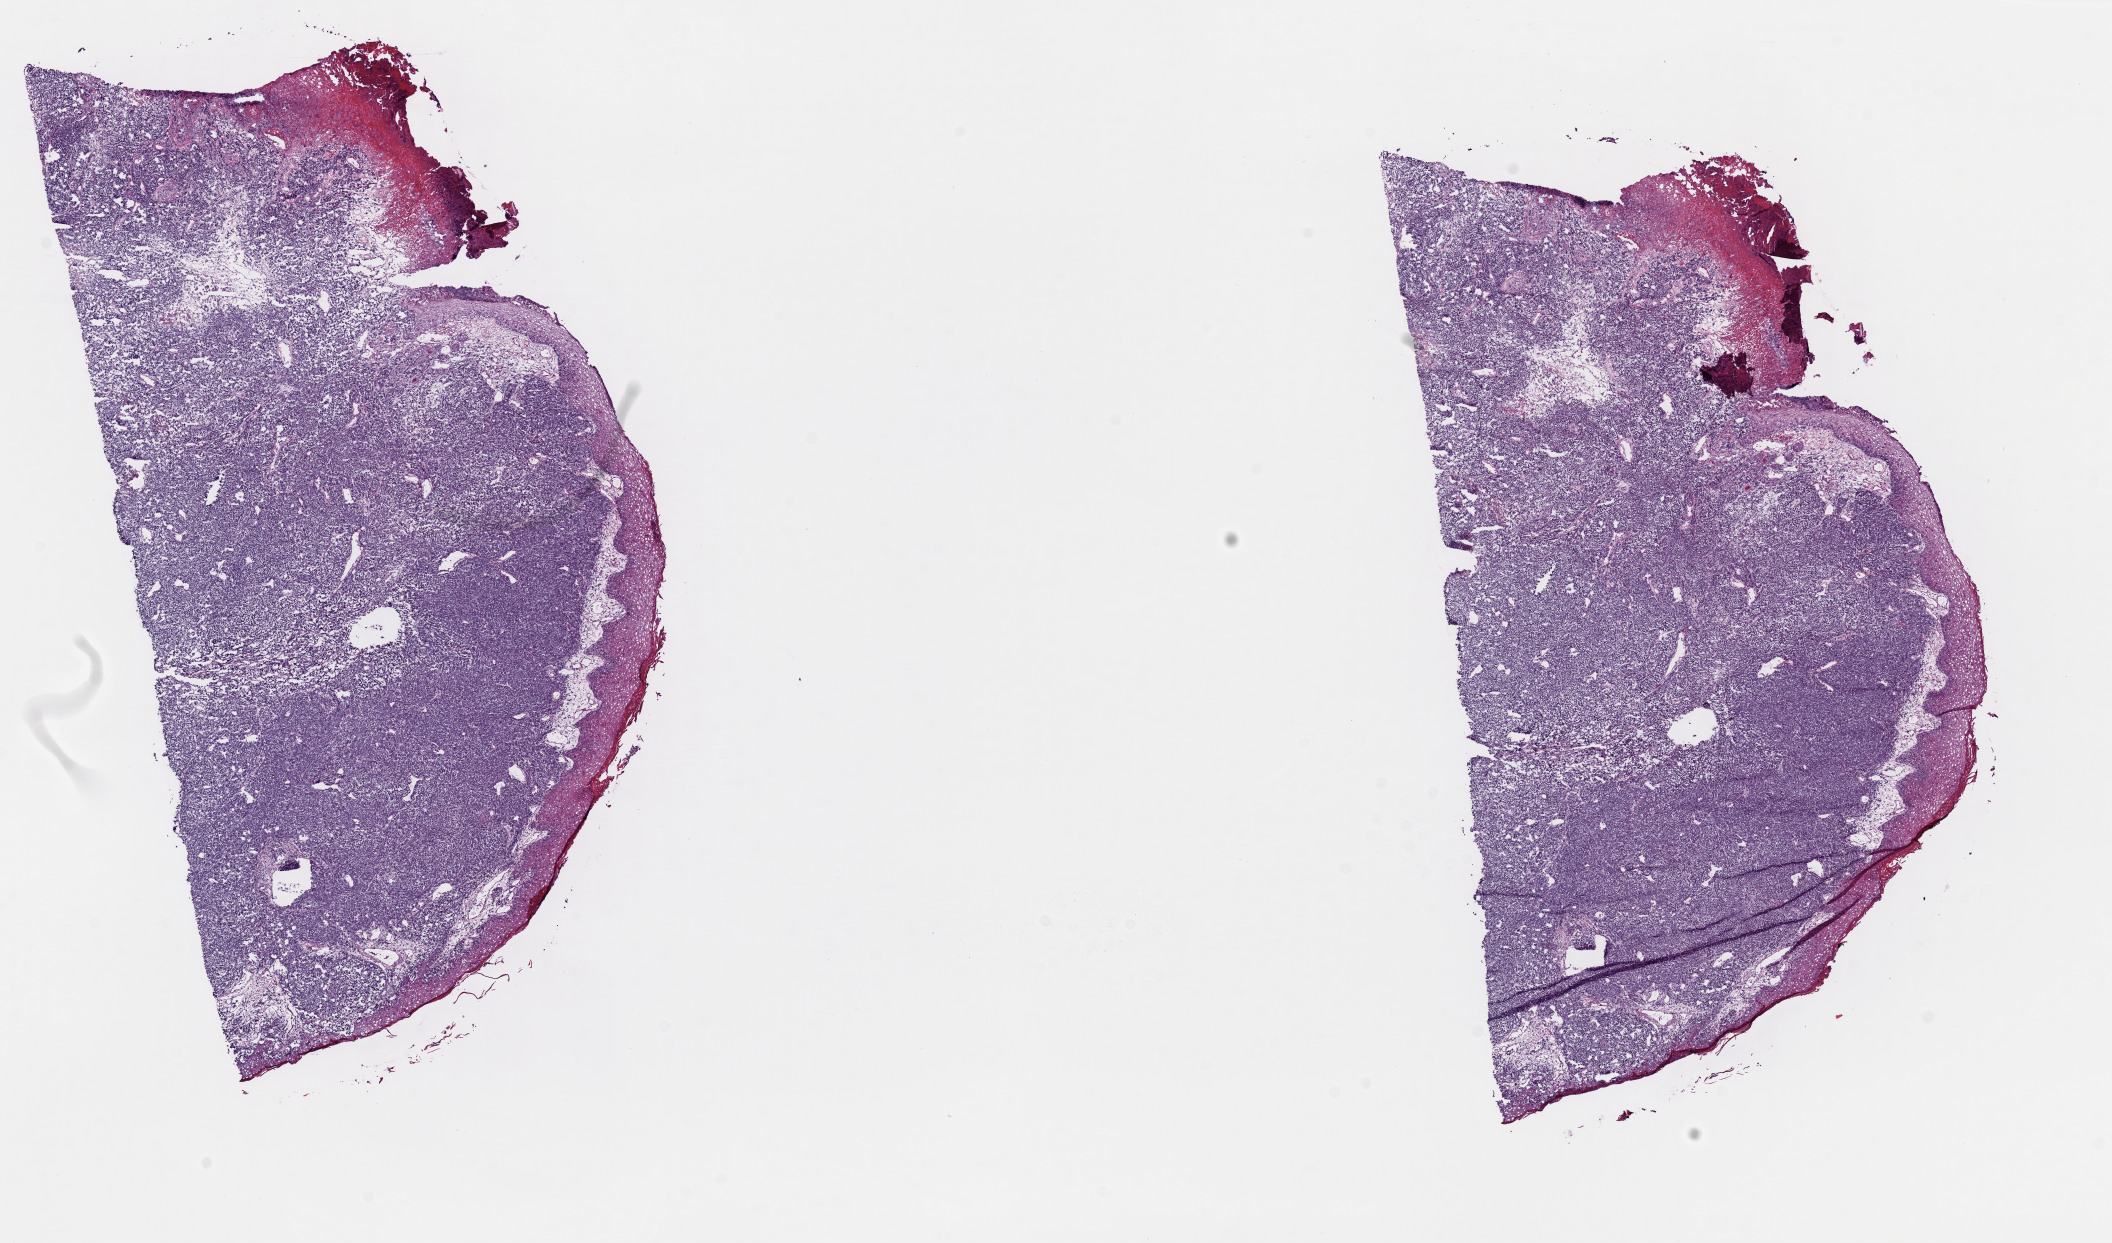
Digitized H&E tissue section (whole slide), a low-resolution overview of the entire scanned area, about 16.7 x 9.8 mm; frozen section from the top of the tissue portion; skin, primary tumour sample. Patient: male, age at initial diagnosis 43 years. Slide review estimates, as recorded: tumour cells 92%, tumour nuclei 92%, normal cells 8%, stromal cells 0%, necrosis 0%. Infiltration values recorded for this section: lymphocyte infiltration 0%, monocyte infiltration 0%, neutrophil infiltration 0%.
AJCC pathologic stage: IIIA (5th edition). Histologic diagnosis: Malignant melanoma, NOS. TNM: T4b N1a M0.